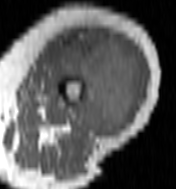
MRI of an extremity soft-tissue mass, one axial slice. Position 47 of 100 along the scan axis. MR volume resampled by the dataset authors to the PET/CT grid (not the native acquisition matrix). 3.27 mm slice thickness. 176 × 189 image matrix, field of view 172 × 185 mm. Female patient. From the clinical record (not read from this slice): histological type: undifferentiated – high grade; grade: high; site of the primary tumour: left thigh.
Annotated regions visible in this slice (expert contour drawn on MRI and transferred to this co-registered scan by the dataset authors):
- gross tumour volume including surrounding oedema: box from (x=53, y=32) to (x=143, y=138) px
- gross tumour volume (mass): (x=57, y=34)–(x=141, y=138)